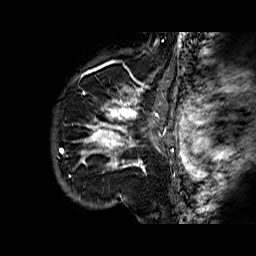
Breast MRI (dynamic contrast-enhanced), one sagittal slice; slice 52 of 60 in the series (ordered by position); dynamic contrast-enhanced series, time point 2 of 6 at this slice position (early post-contrast); 1.5 T; TE 6.3 ms, TR 32.4 ms; 4 mm slice thickness; 256 × 256 image matrix. Female patient. Case-level facts recorded for this patient, not image findings: setting: breast cancer imaged before/during neoadjuvant chemotherapy; receptor status: HR-positive, HER2-negative.
Annotated regions visible in this slice (semi-automatic segmentation, software-assisted and operator-edited):
- analysis volume of interest (the breast-tissue region the enhancement analysis was run in; not a lesion): bounding box (x1, y1, x2, y2) in pixels: (69, 72, 177, 183)
- tumour enhancement mask (voxels above the 100 % enhancement threshold inside the analysis volume of interest): (79, 74, 174, 169)